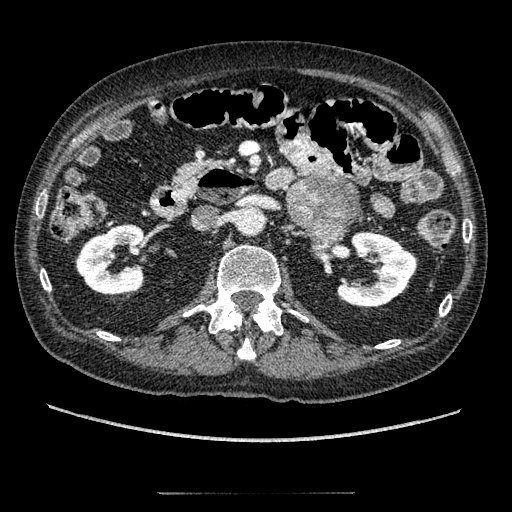
Contrast-enhanced abdominal CT, one axial slice. Slice 93 of 274 in the series (ordered by position). Reconstruction kernel STANDARD. Intravenous contrast given. Soft-tissue window (W 400 / L 40 HU). 1.25 mm slice thickness. 512 × 512 image matrix, field of view 381 × 381 mm. Male patient, age 69 years. Case-level facts recorded for this patient, not image findings: diagnosis: adrenocortical carcinoma; tumour side: left adrenal; tumour size at pathology: 6.1 cm; Ki-67 index: 10 %; stage (as recorded): 3.
Structures marked on this image (semi-automatic segmentation, software-assisted and operator-edited):
- mass: bounding box (x1, y1, x2, y2) in pixels: (289, 179, 359, 242)